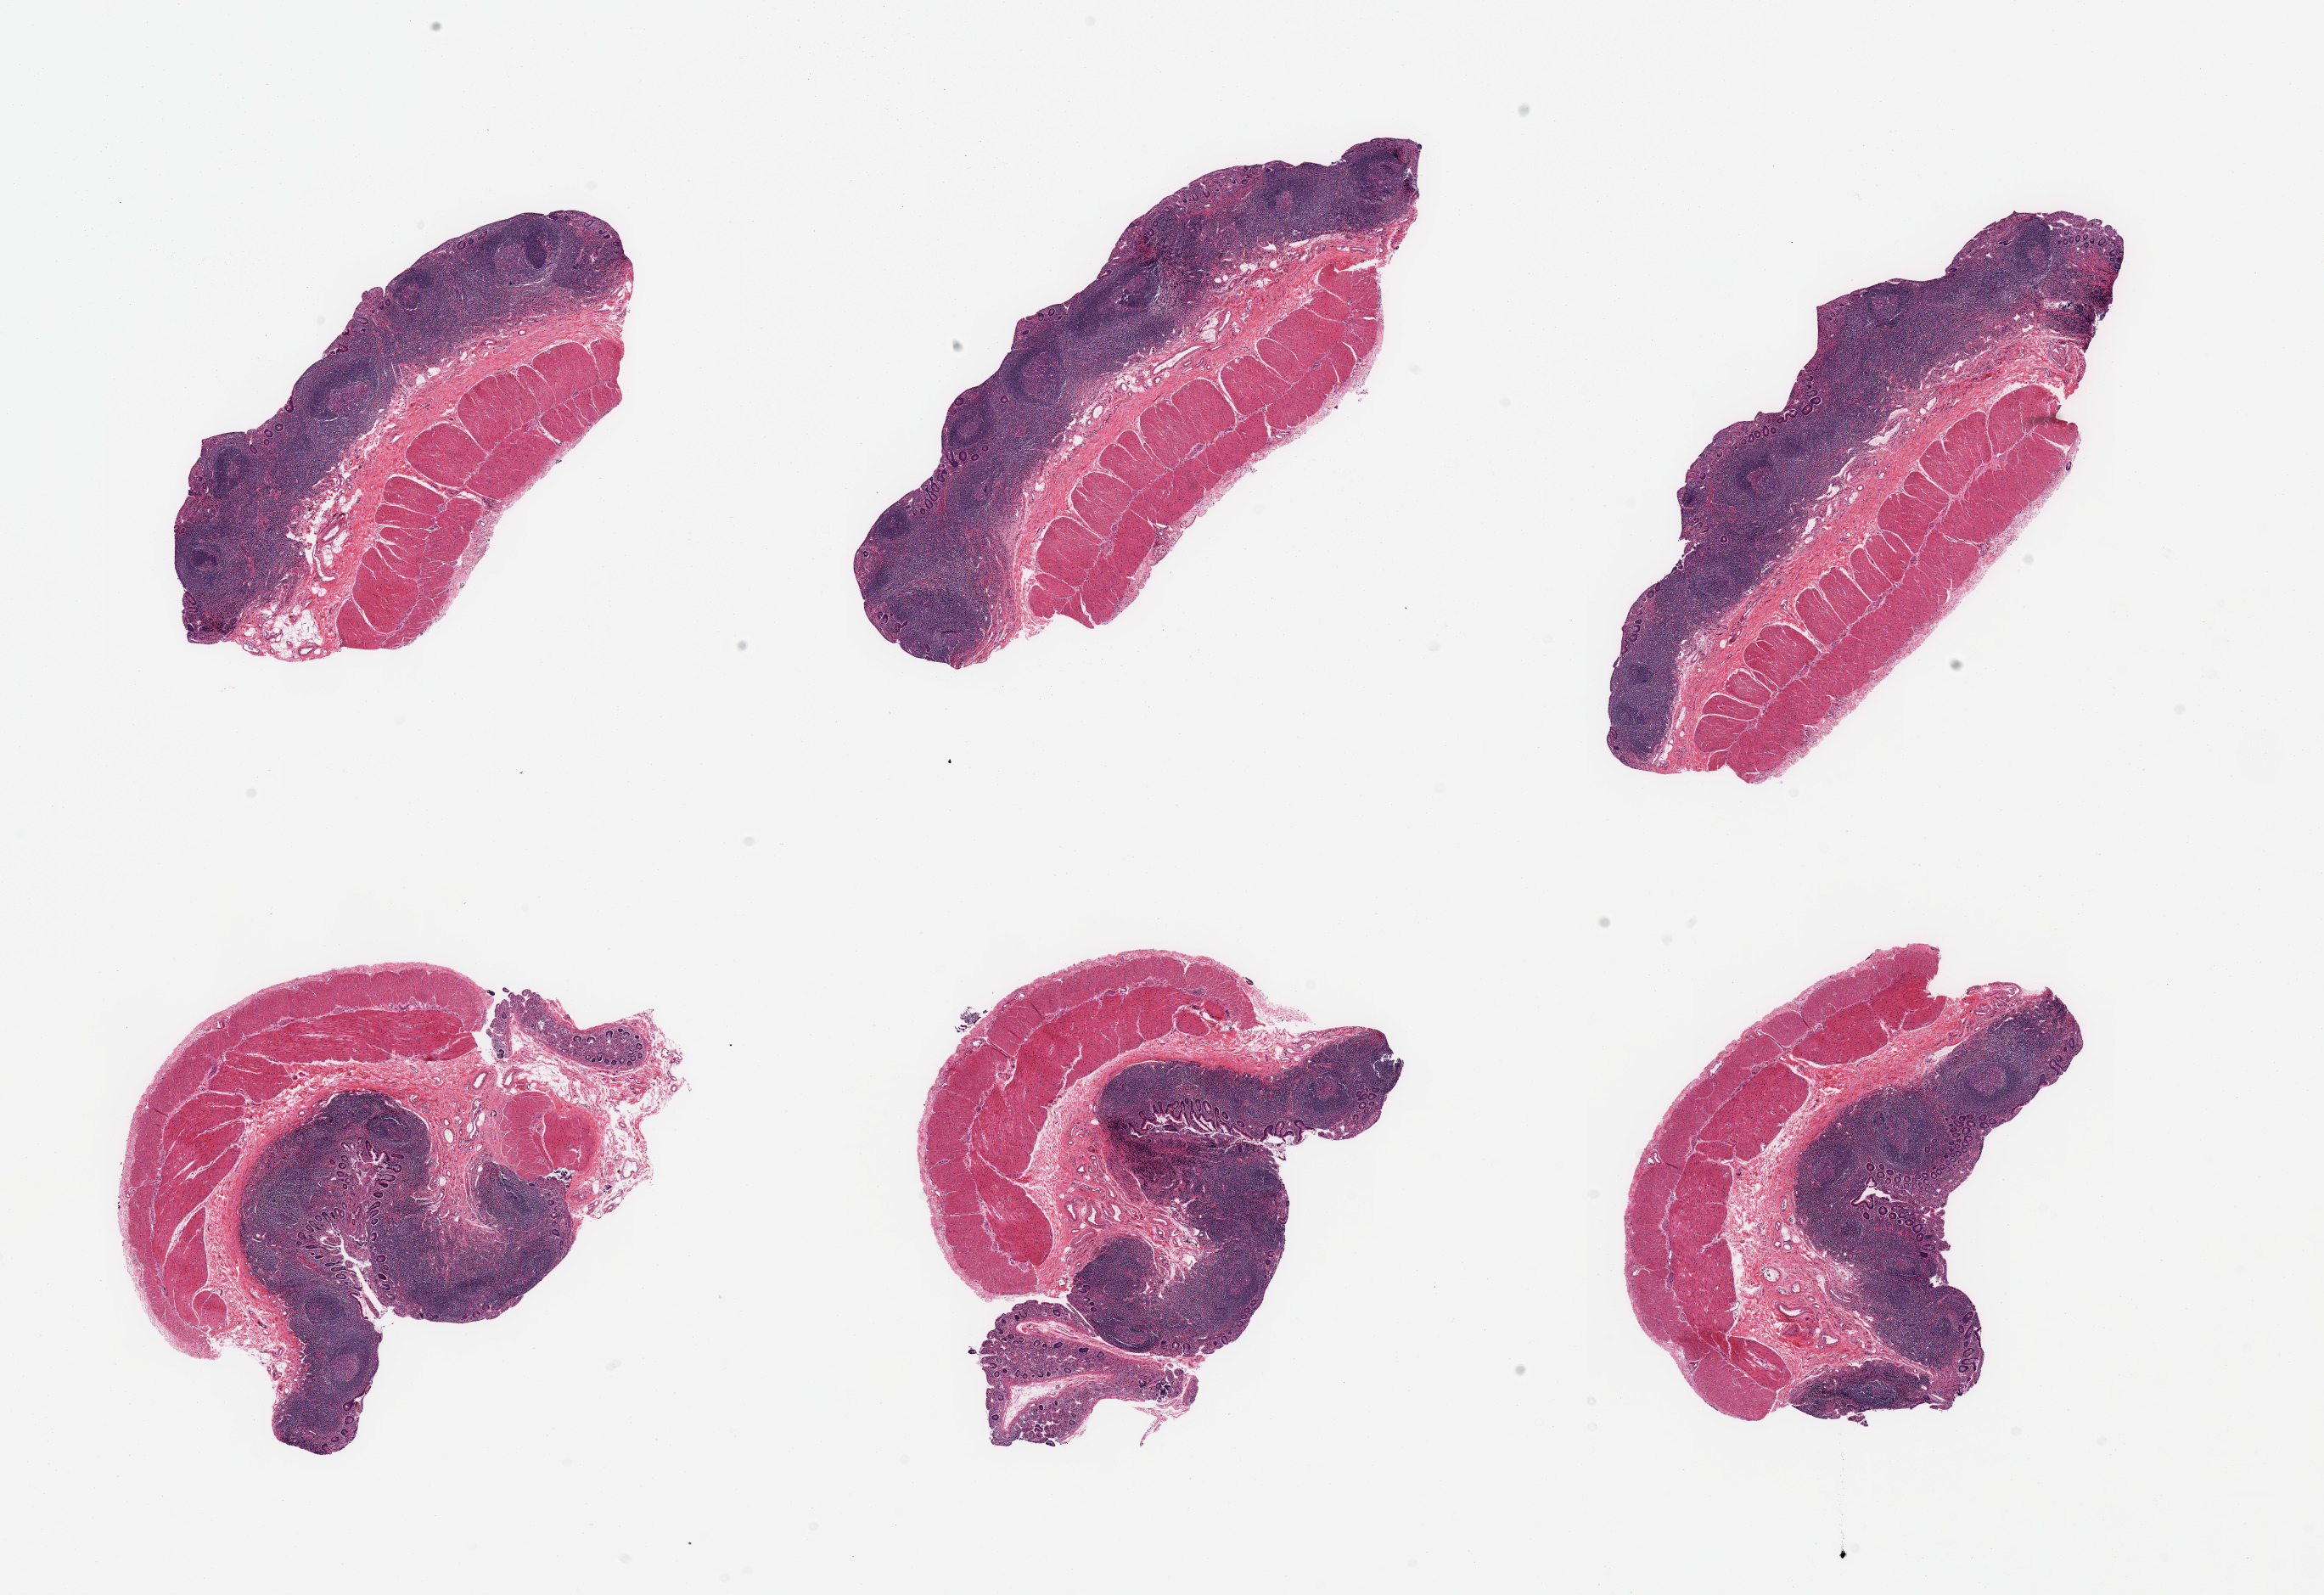
Digitized H&E-stained section, low-resolution overview of the scanned area, about 21.7 x 14.9 mm. PAXgene-fixed, paraffin-embedded tissue. Section of ileum (target tissue). Tissue donor sample. Donor: male.
Review note (as recorded): 6 pieces; target abundant mucosal lymphoid tissue; non-target muscularis present.